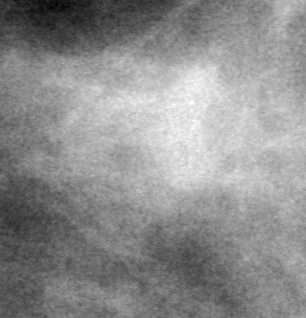
Cropped region of a digitized screen-film mammogram centred on a radiologist-marked abnormality, left breast, MLO view, BI-RADS breast density category 3 (scale 1–4).
- Mass, shape irregular, margins obscured; BI-RADS assessment category 0 (incomplete: needs additional imaging); subtlety rating 3 on a 1 (subtle) to 5 (obvious) scale; pathology result (as recorded, not read from the image): benign.